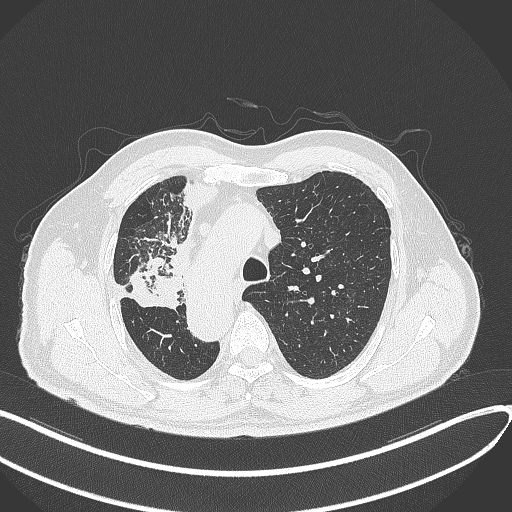
Chest CT, one axial slice; slice 232 of 300 in the series (ordered by position); lung window (W 1500 / L -600 HU); 1 mm slice thickness; 512 × 512 image matrix. Patient: male, 67 years. Case-level facts recorded for this patient, not image findings: clinical TNM (as recorded): T2a N0 M0.
Structures marked on this image (bounding box drawn by a radiologist):
- lung tumour (recorded histology: squamous cell carcinoma): box from (x=129, y=254) to (x=185, y=311) px